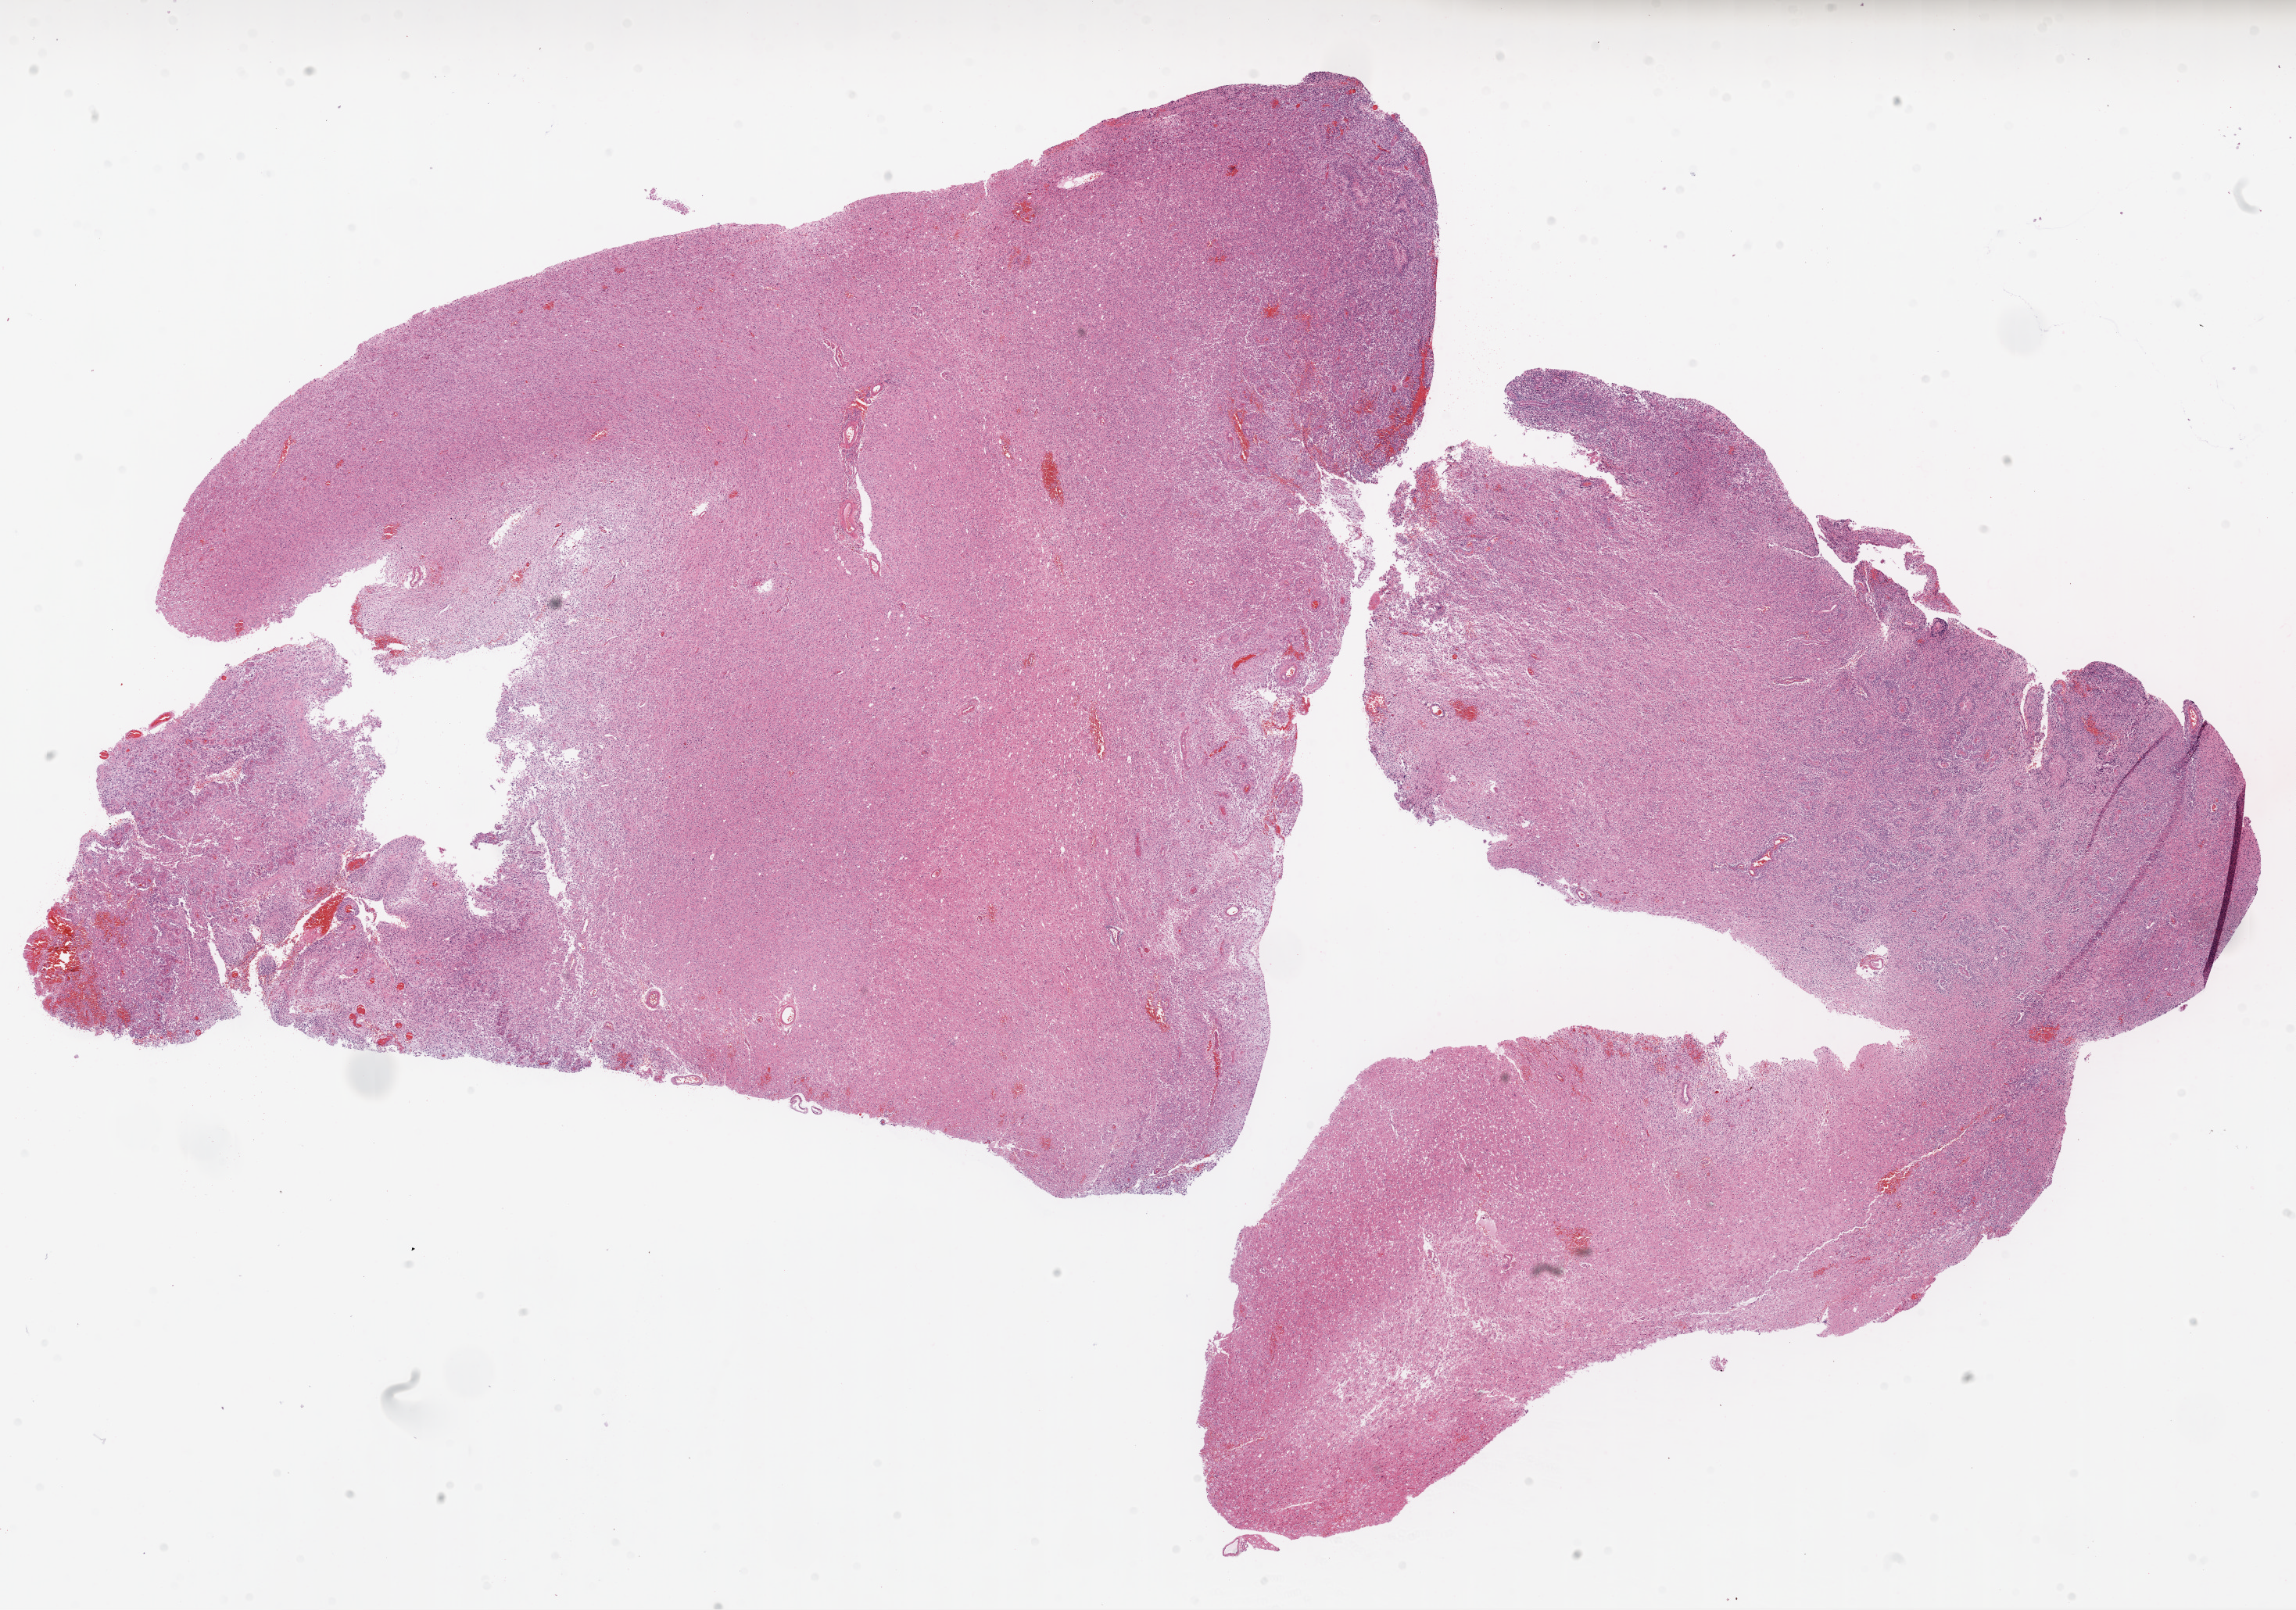
Digitized H&E tissue section (whole slide), a low-resolution overview of the entire scanned area, about 23.7 x 16.6 mm (slide scanned at 20x). FFPE section. Primary tumour sample from the brain. Patient: male, age at initial diagnosis 51 years.
Pathologic diagnosis: Glioblastoma.